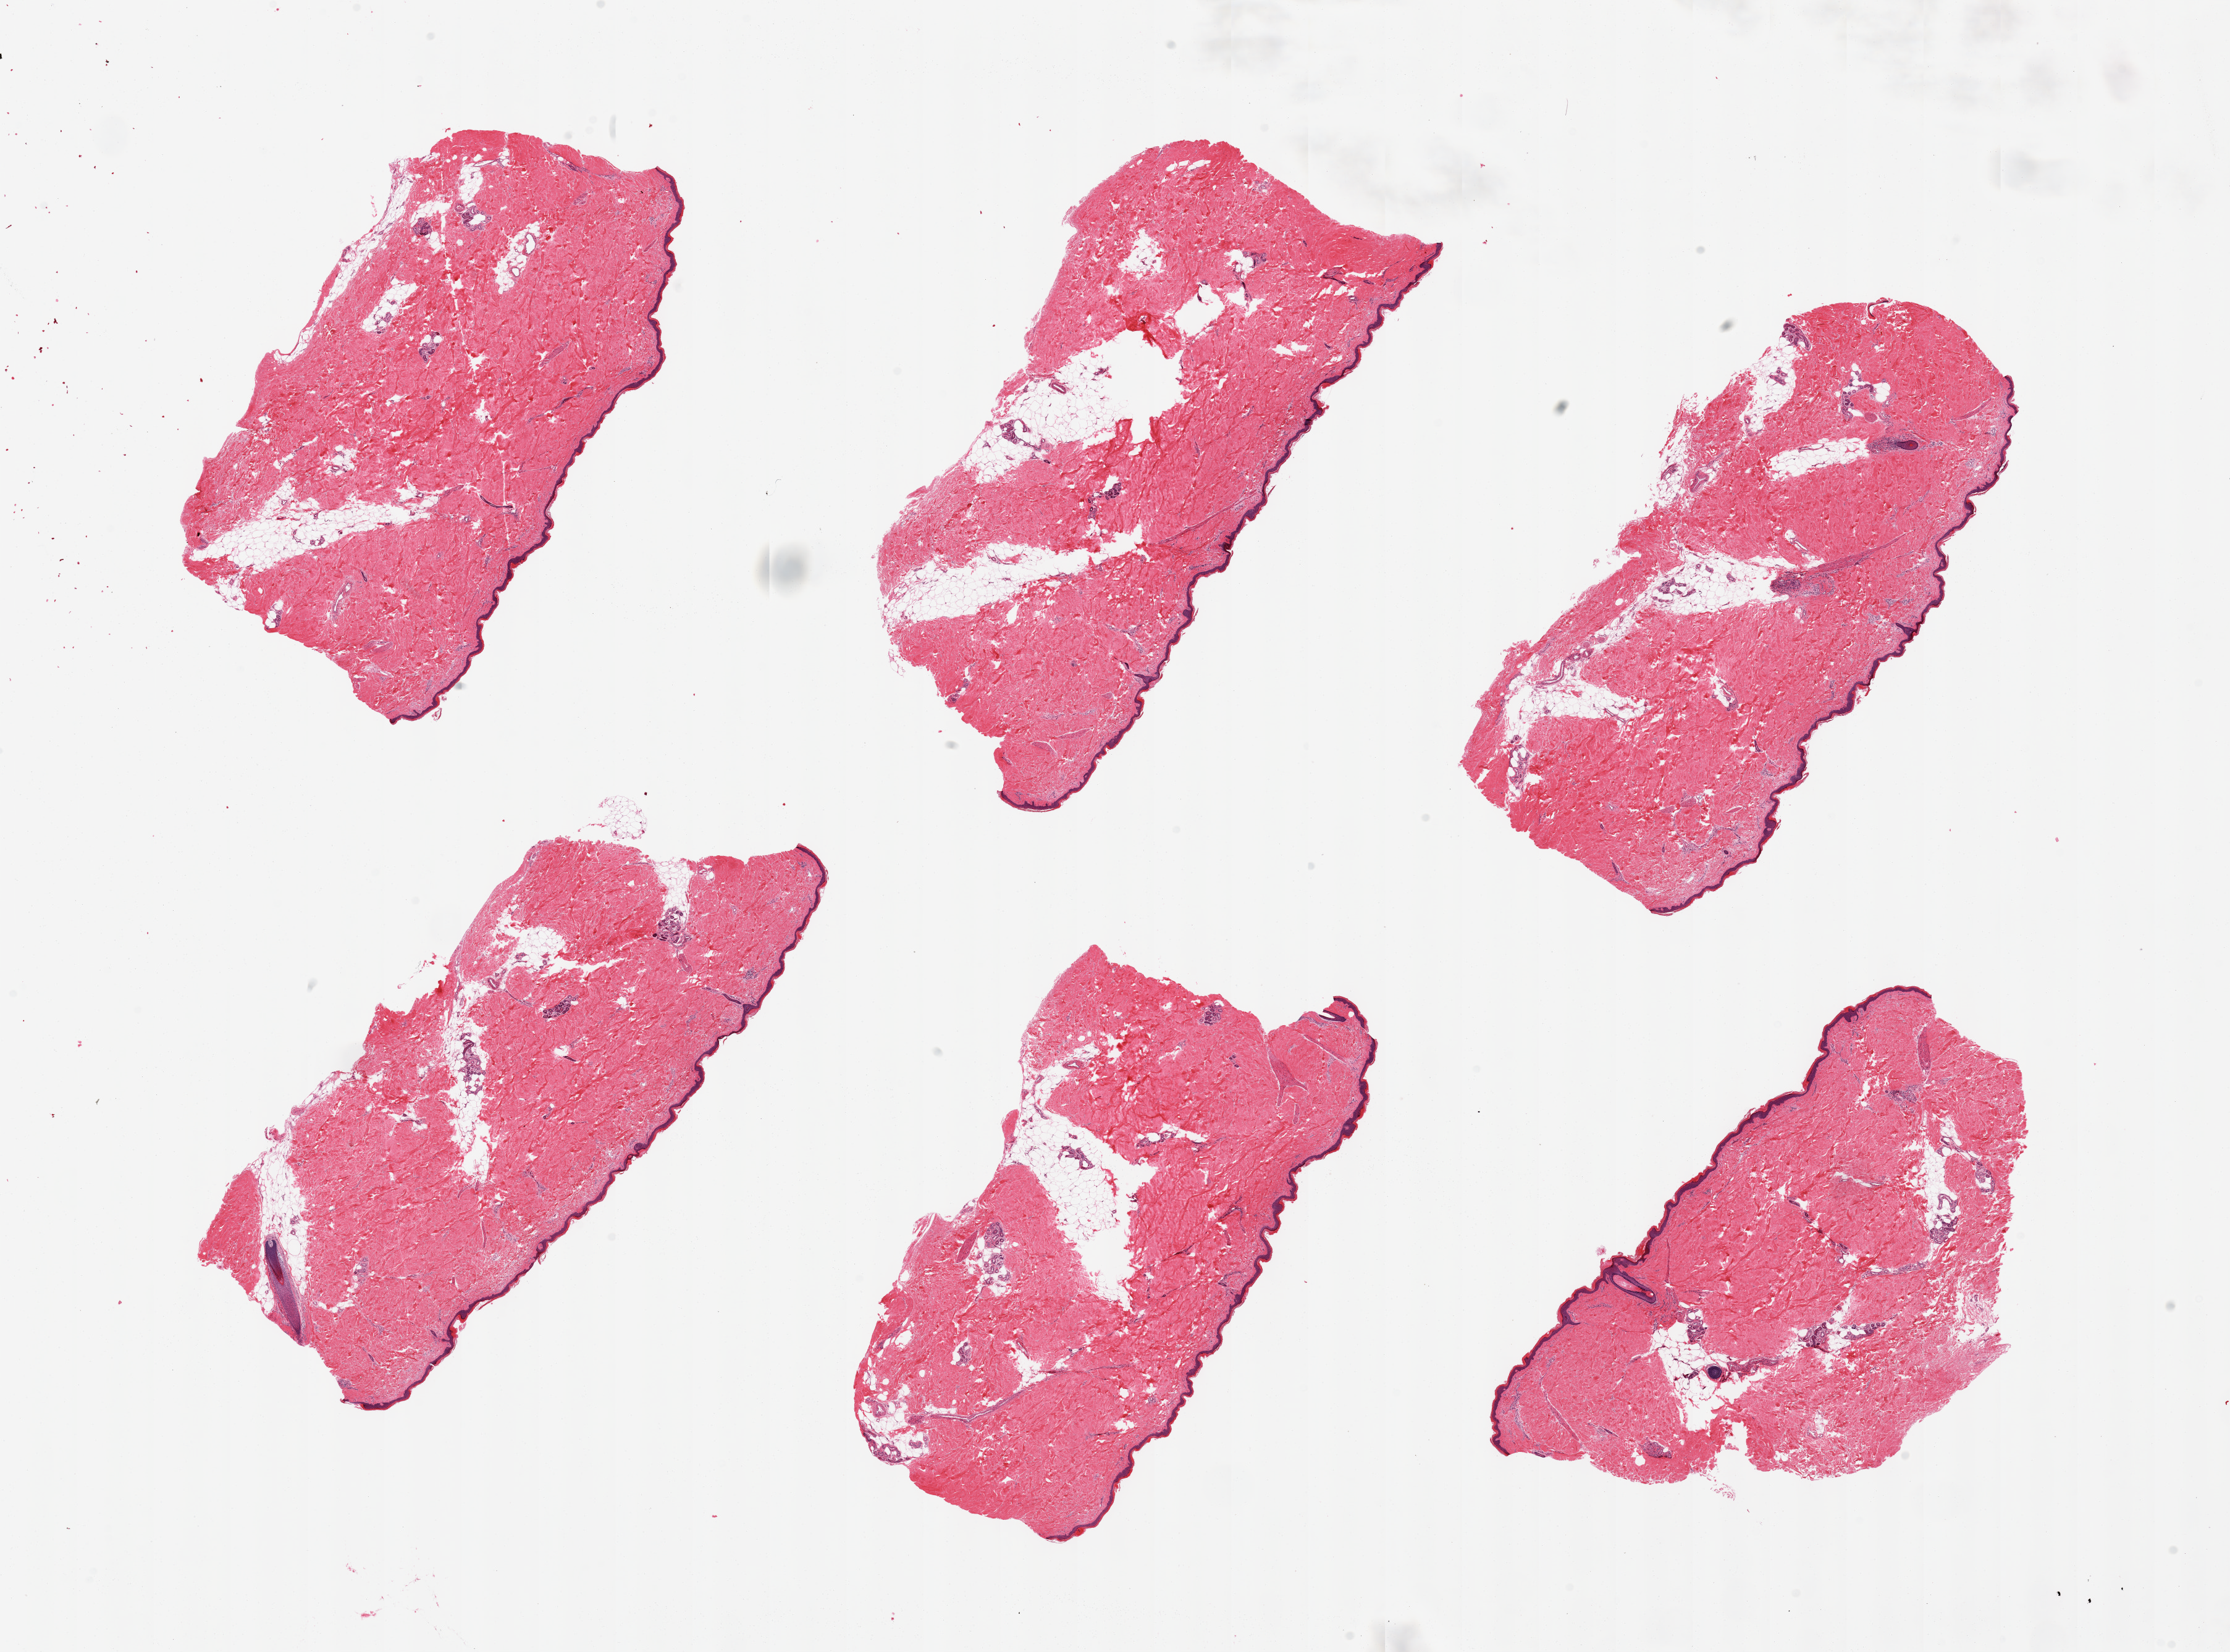
Digitized H&E-stained section, brightfield, shown as a low-resolution overview of the whole scanned area (about 28.5 x 21.2 mm). Donor: male.
Specimen: PAXgene-fixed paraffin-embedded (PFPE) section; sampled site (target tissue): skin of lower leg; donor tissue sample.